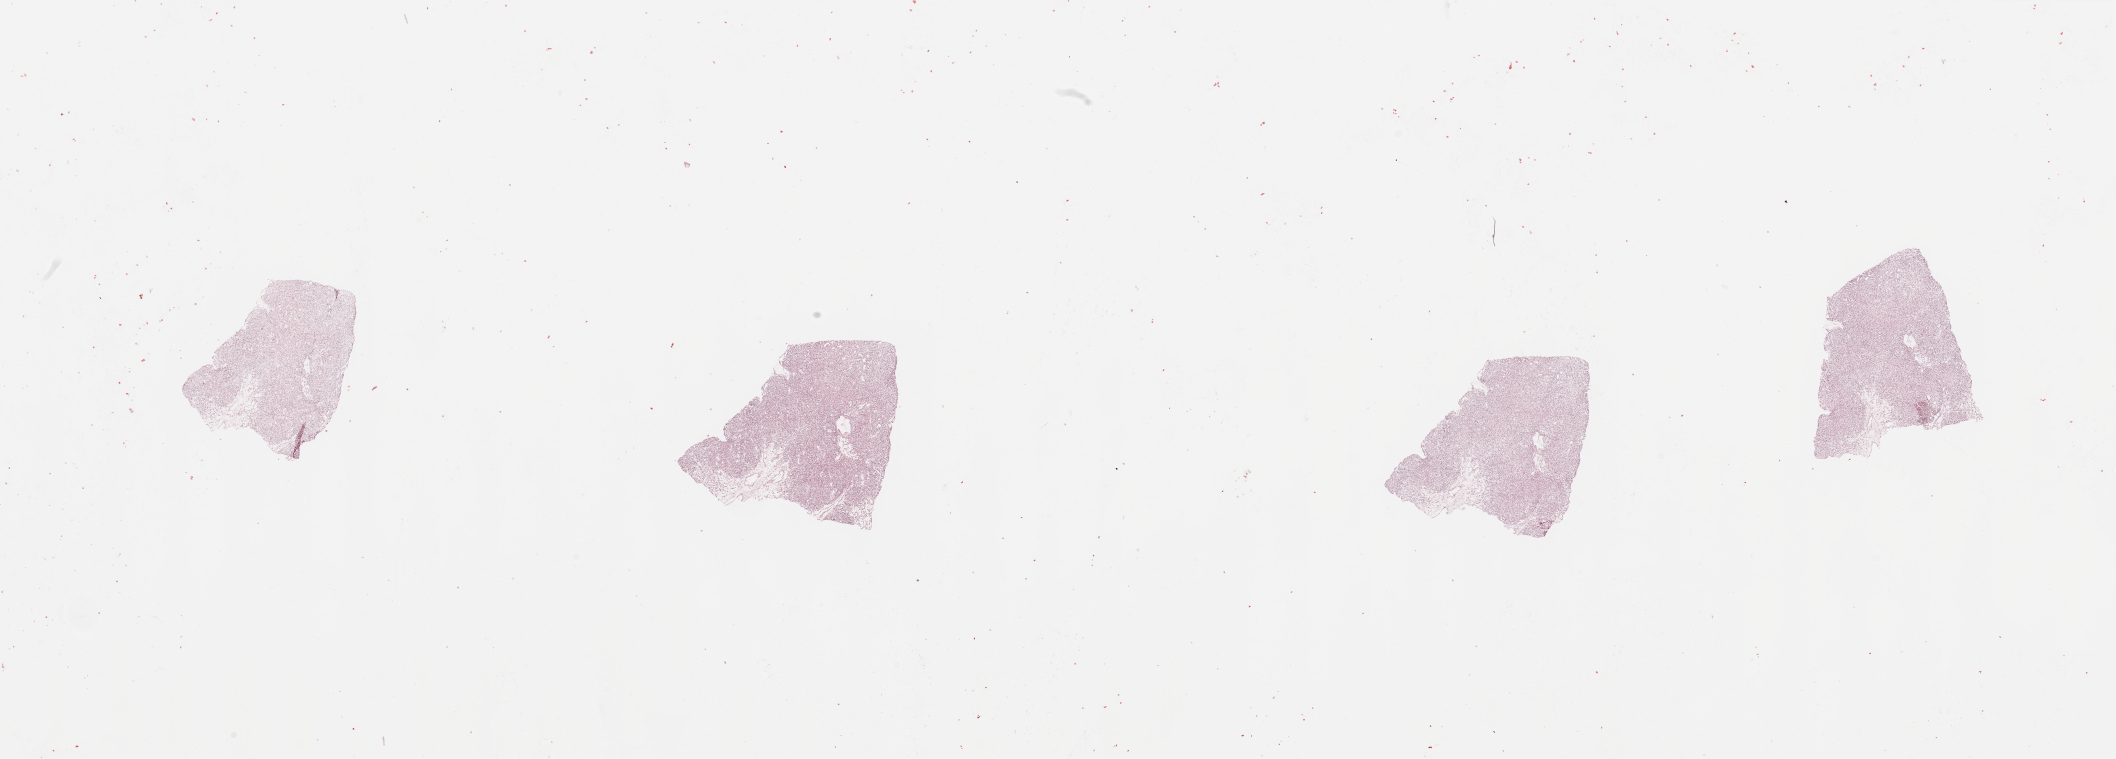
Digitized H&E tissue section (whole slide), a low-resolution overview of the entire scanned area, about 33.5 x 12.0 mm (from a 20x scan); tumour tissue sample, kidney. Female, 64 y/o. Histologic grade: G2 (moderately differentiated).
AJCC pathologic stage: III. Diagnosis: Renal cell carcinoma, NOS.